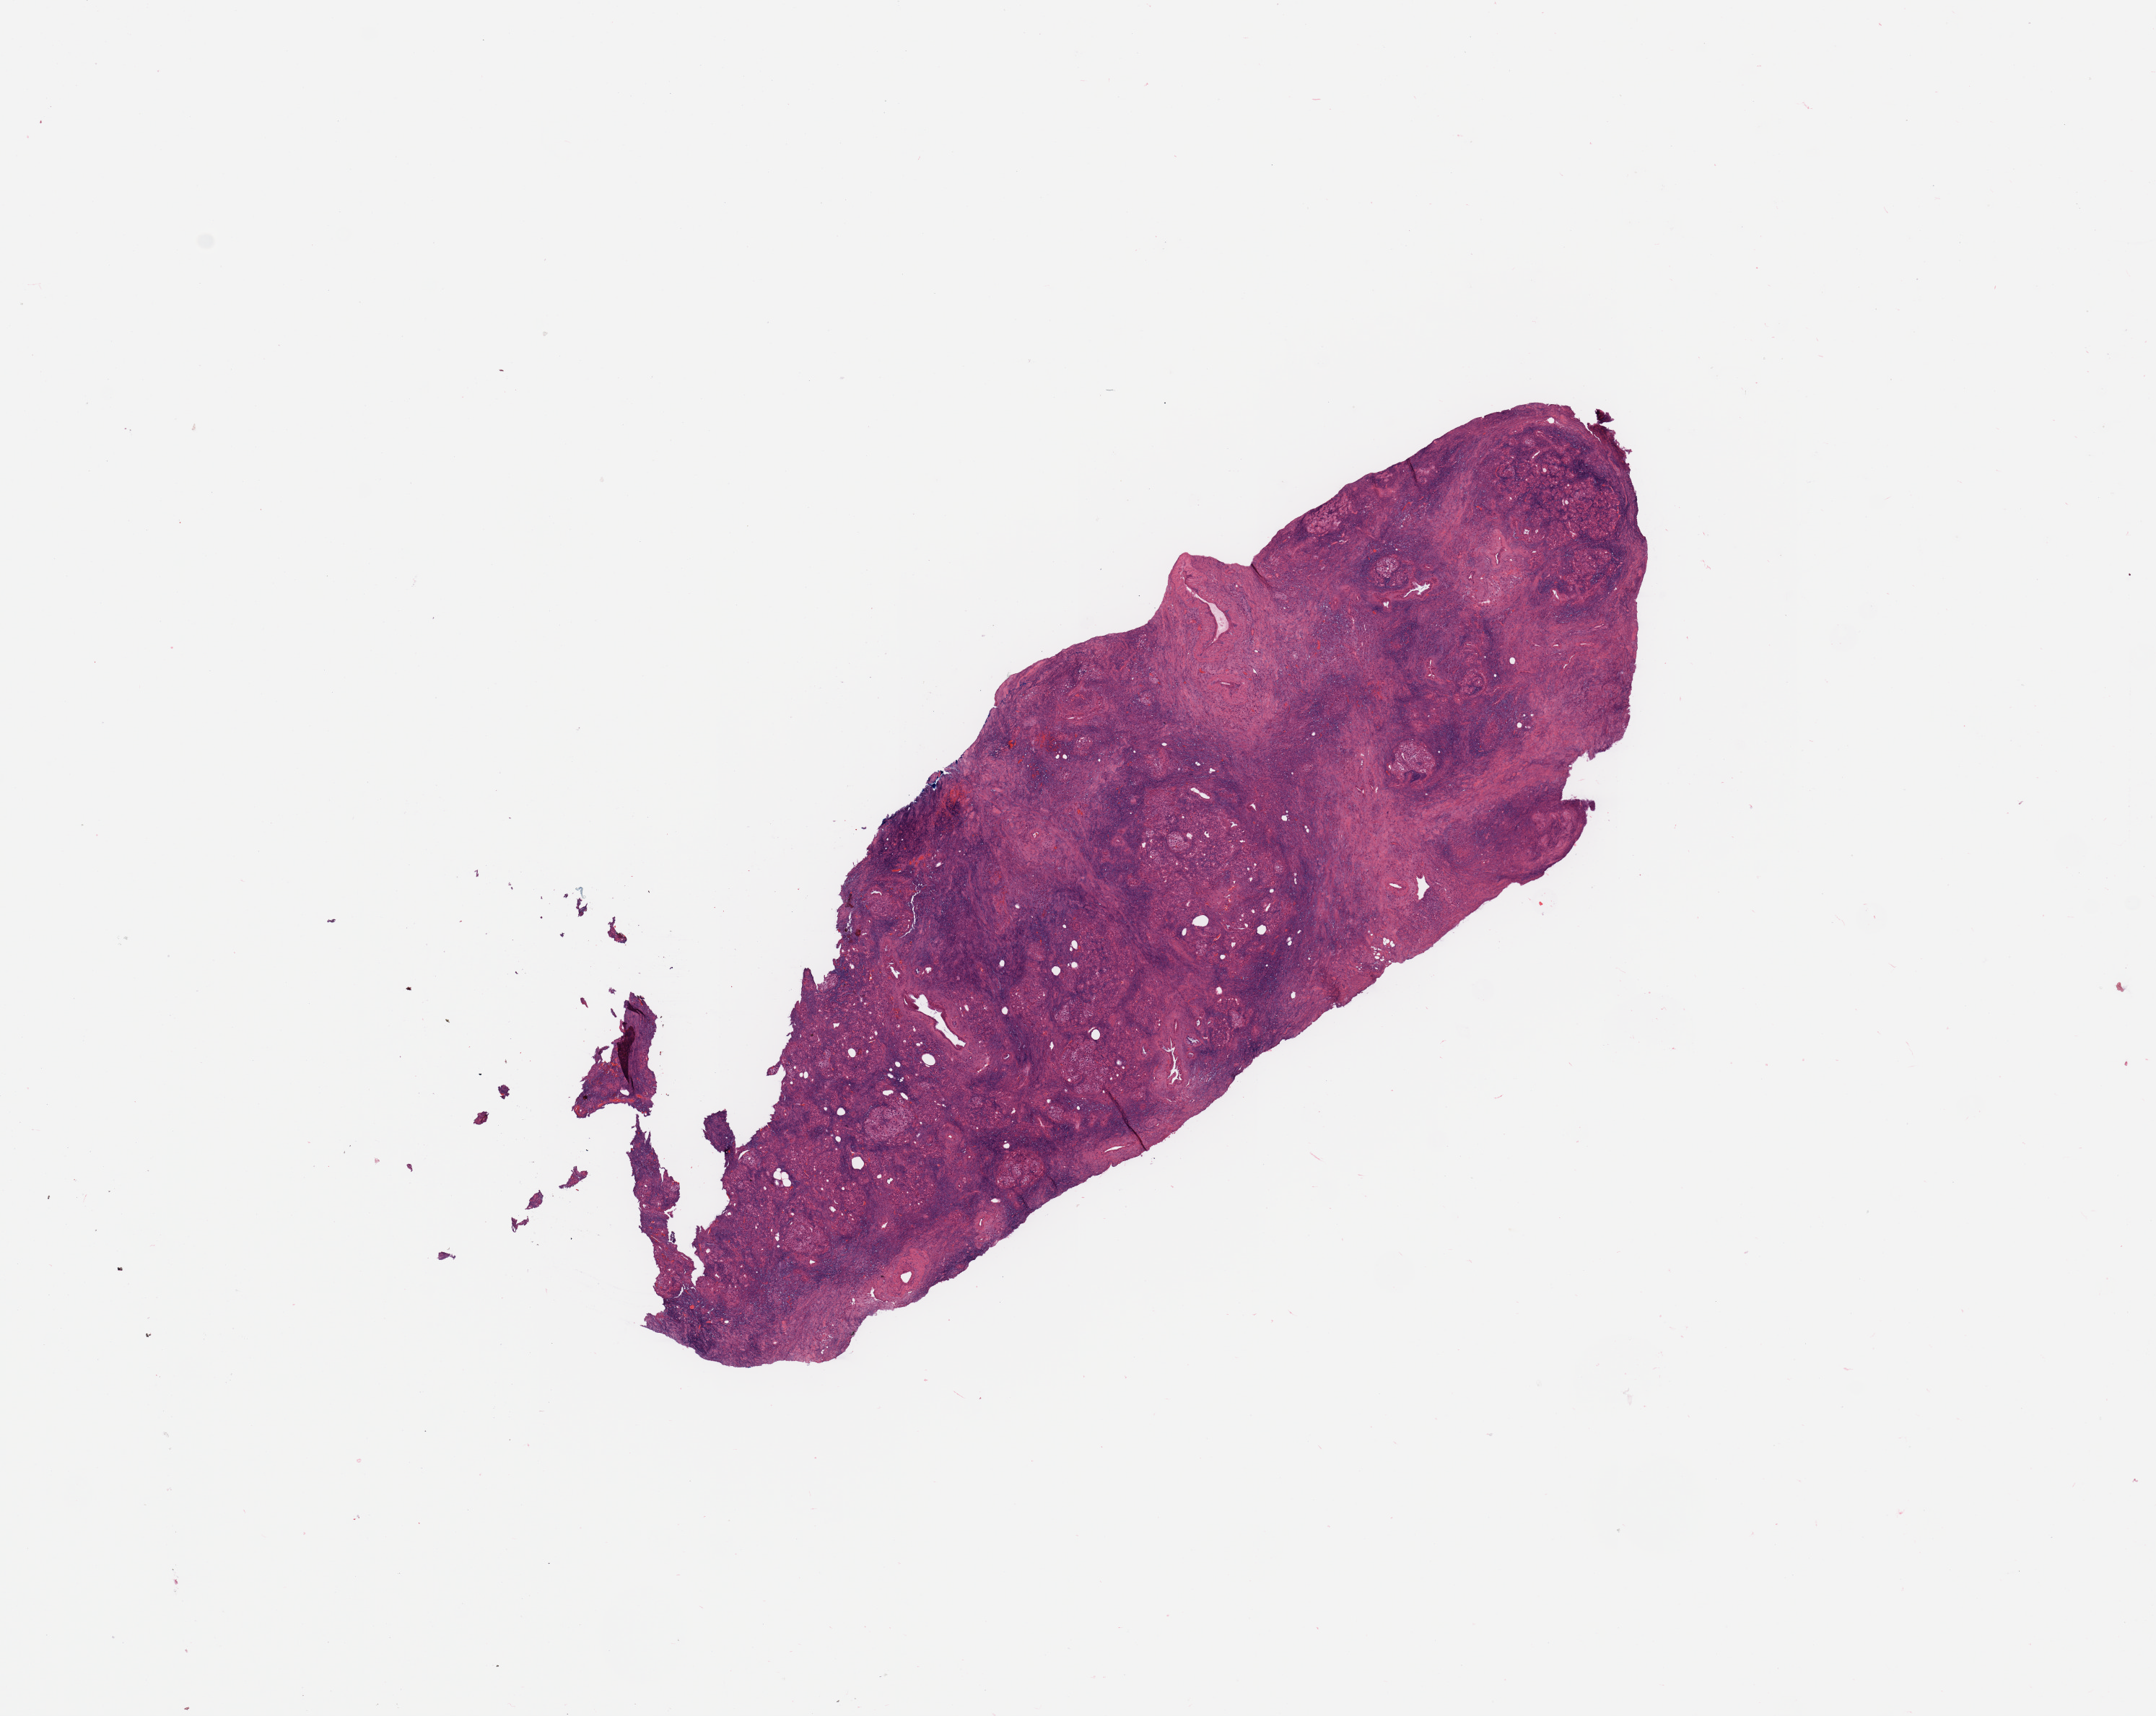
H&E whole-slide image, a low-resolution overview of the entire scanned area, about 11.8 x 9.4 mm (acquisition: 20x scan). Normal (non-tumour) tissue sample, sampled site: pancreas. Patient: male, age 71 years.
• this section: normal (non-tumour) tissue from the same patient
• patient diagnosis: Infiltrating duct carcinoma, NOS